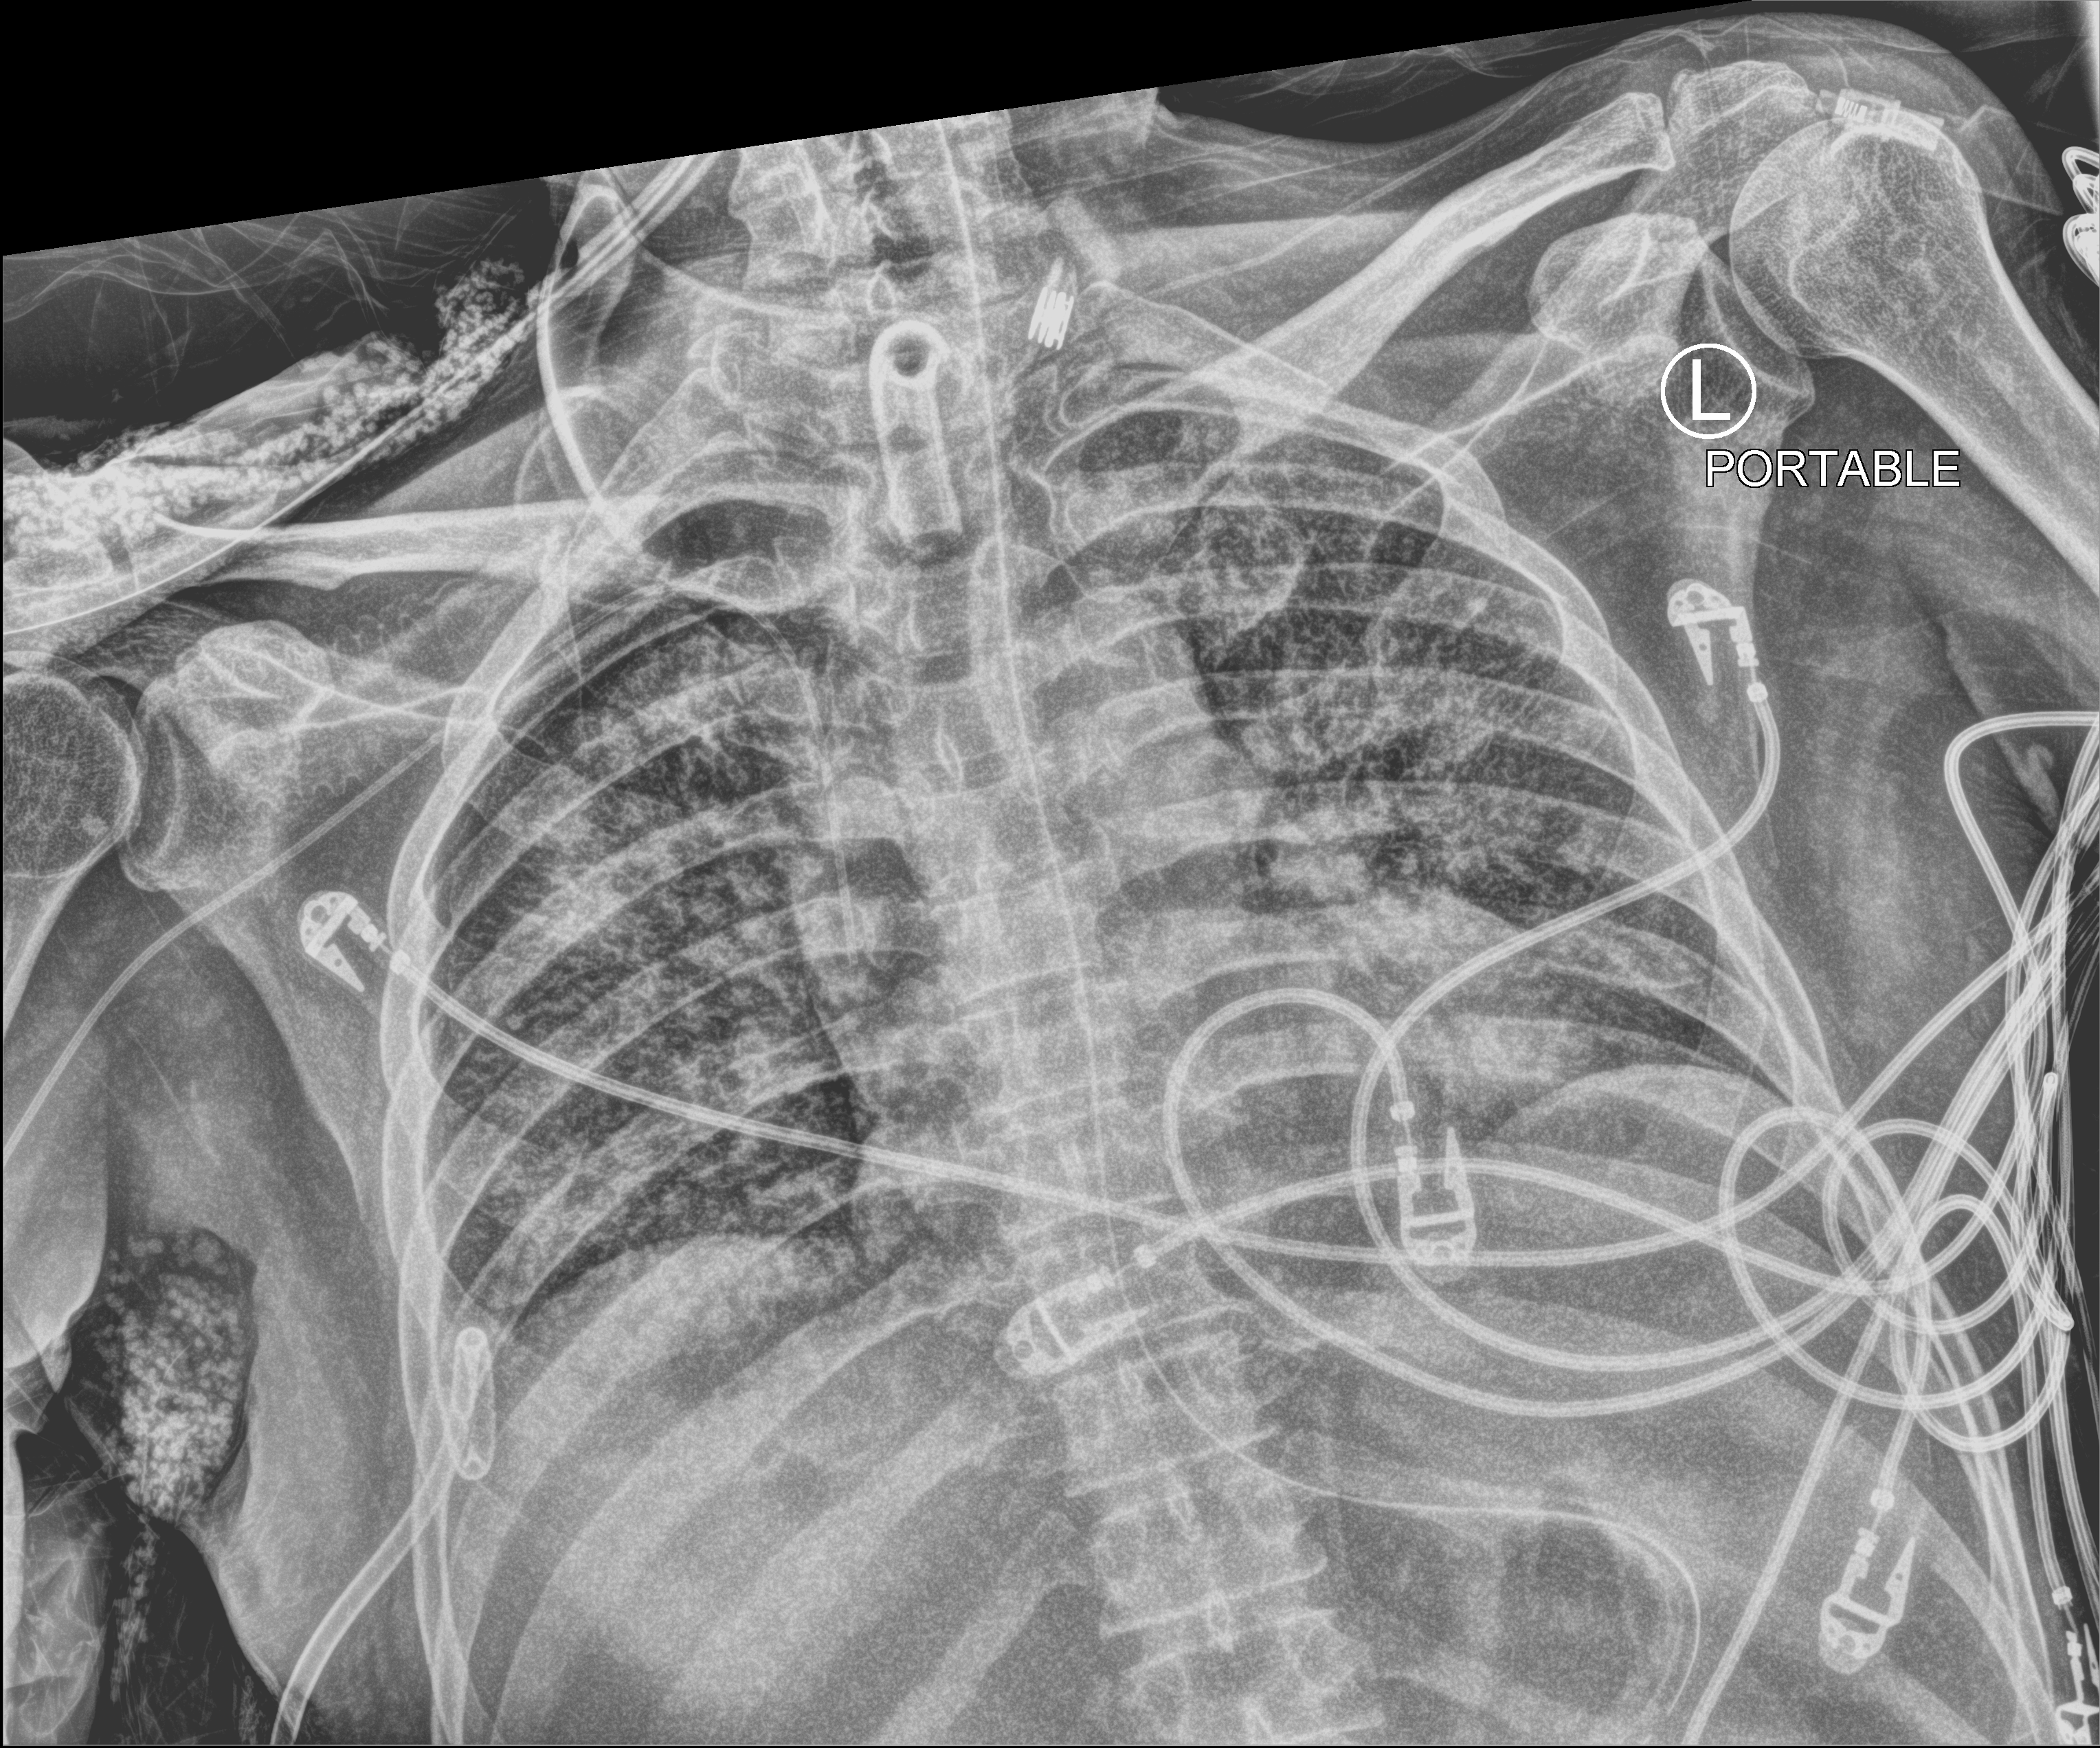
Bedside chest radiograph (computed radiography); anteroposterior (AP) projection. Patient hospitalised with COVID-19; male, aged 18–59 years.
Admission-level facts for this patient (not findings on this image; timing relative to this image not recorded): diabetes (admission record): no; admitted to intensive care during this hospital stay: yes; length of hospital stay: 77 days.